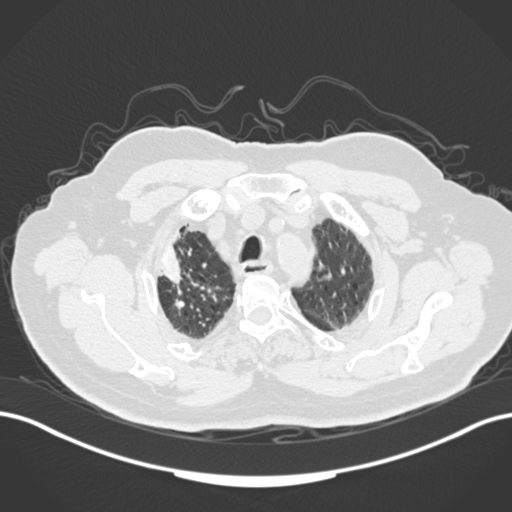
Chest CT, one axial slice; reconstruction kernel B30f; 120 kVp; lung window (W 1500 / L -600 HU); 512 × 512 image matrix. Male patient, age 72 years. Case-level facts recorded for this patient, not image findings: clinical TNM (as recorded): T1a N0 M0.
Outlined on this slice (bounding box drawn by a radiologist):
- lung tumour (recorded histology: squamous cell carcinoma): bounding box (x1, y1, x2, y2) in pixels: (160, 240, 194, 311)